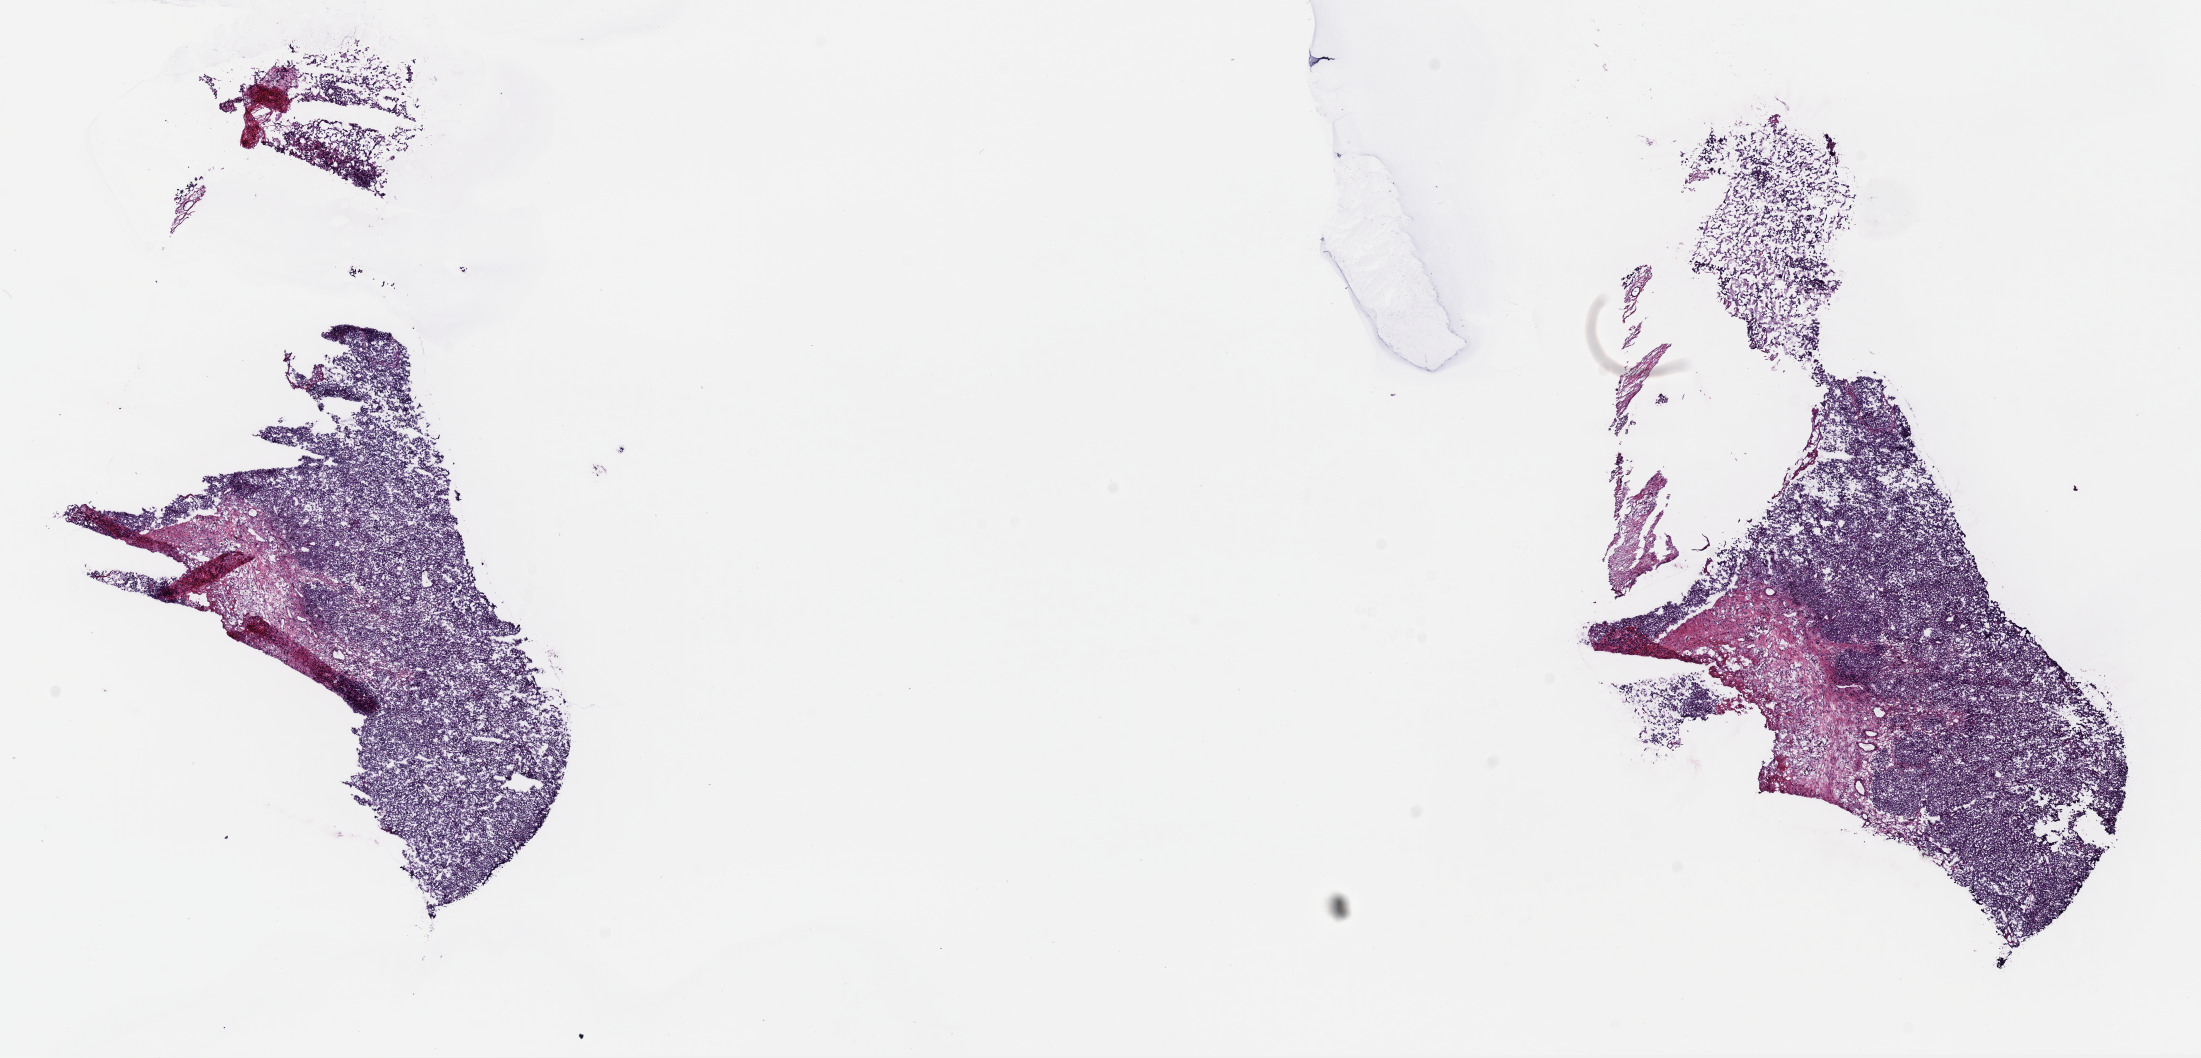
Digitized Hematoxylin and eosin (H&E) stained tissue section (whole slide) — whole scanned area (about 17.4 x 8.4 mm, from a 40x scan) shown as a low-resolution overview; frozen section from the top of the tissue portion; metastatic tumour sample, sampled site: lymph node. Patient: female, age at initial diagnosis 75 years. Composition of this section per pathologist review: tumour cells 85%, tumour nuclei 90%, normal cells 0%, stromal cells 15%, necrosis 0%. Infiltration values recorded for this section: lymphocyte infiltration 0%, monocyte infiltration 0%, neutrophil infiltration 0%.
This section: metastatic tumour tissue. Patient diagnosis: Malignant melanoma, NOS.